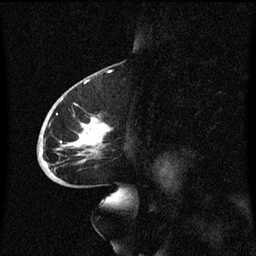
Breast MRI (dynamic contrast-enhanced), one sagittal slice; slice 34 of 60 in the series (ordered by position); dynamic contrast-enhanced series, image 2 of 3 at this slice position (ordered by acquisition); 1.5 T; TE 4.2 ms, TR 8.4 ms; 2 mm slice thickness; 256 × 256 image matrix. Patient: female, 68 years. From the clinical record (not read from this slice): setting: breast cancer imaged before/during neoadjuvant chemotherapy; receptor status: triple-negative.
Structures marked on this image (semi-automatic segmentation, software-assisted and operator-edited):
- analysis volume of interest (the breast-tissue region the enhancement analysis was run in; not a lesion): bounding box [x1, y1, x2, y2] px = [38, 94, 114, 173]
- tumour enhancement mask (voxels above the 70 % enhancement threshold inside the analysis volume of interest): [44, 118, 111, 169]